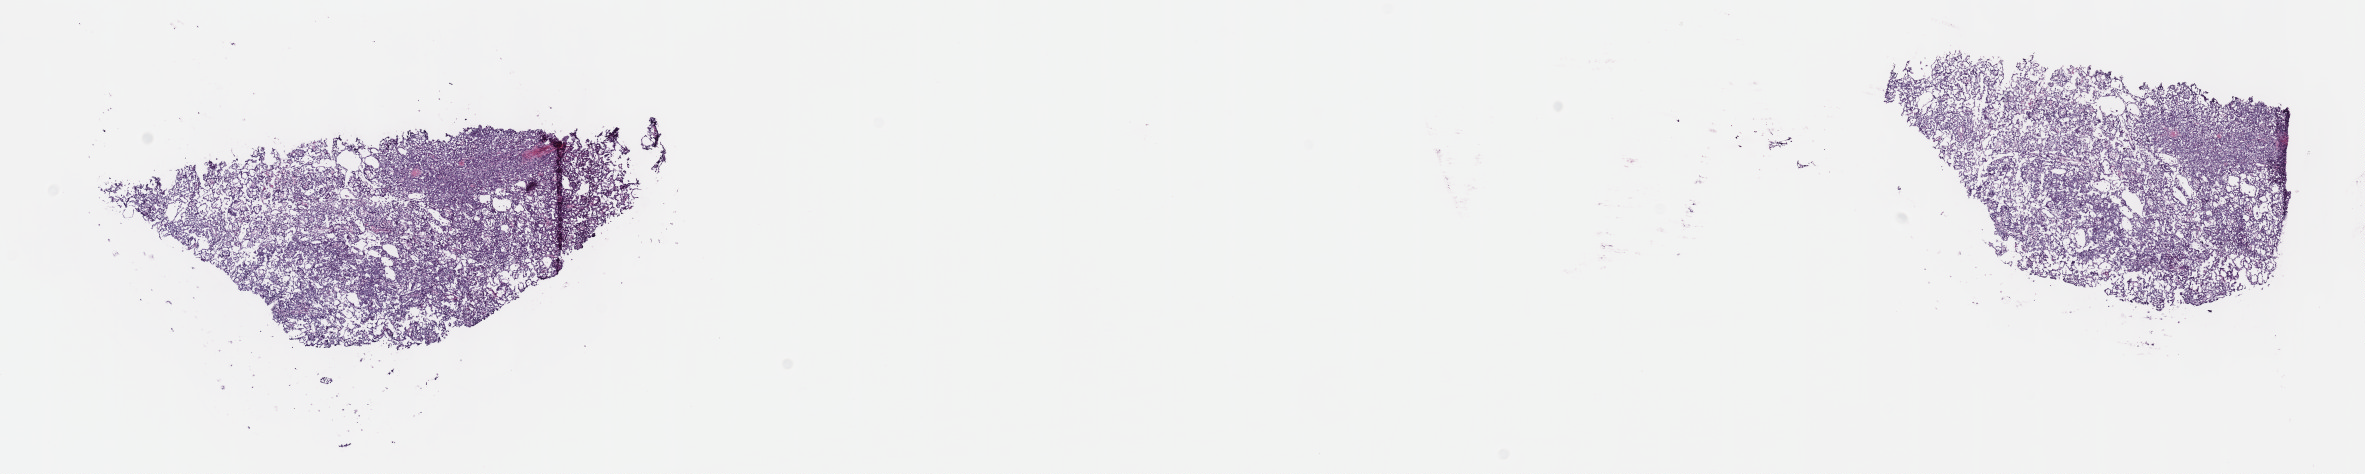
Digitized H&E tissue section (whole slide), low-resolution overview of the scanned area, about 19.1 x 3.8 mm (acquisition: 40x scan); frozen section; primary tumour sample from the kidney. Male patient; age at initial diagnosis 54 years. Composition of this section per pathologist review: tumour cells 100%, tumour nuclei 80%, normal cells 0%, stromal cells 0%, necrosis 0%. Inflammatory infiltration, as recorded: lymphocyte infiltration 1%, monocyte infiltration 3%, neutrophil infiltration 0%.
* AJCC pathologic stage: I (7th edition)
* pathologic diagnosis: Papillary adenocarcinoma, NOS
* TNM: T1a NX M0